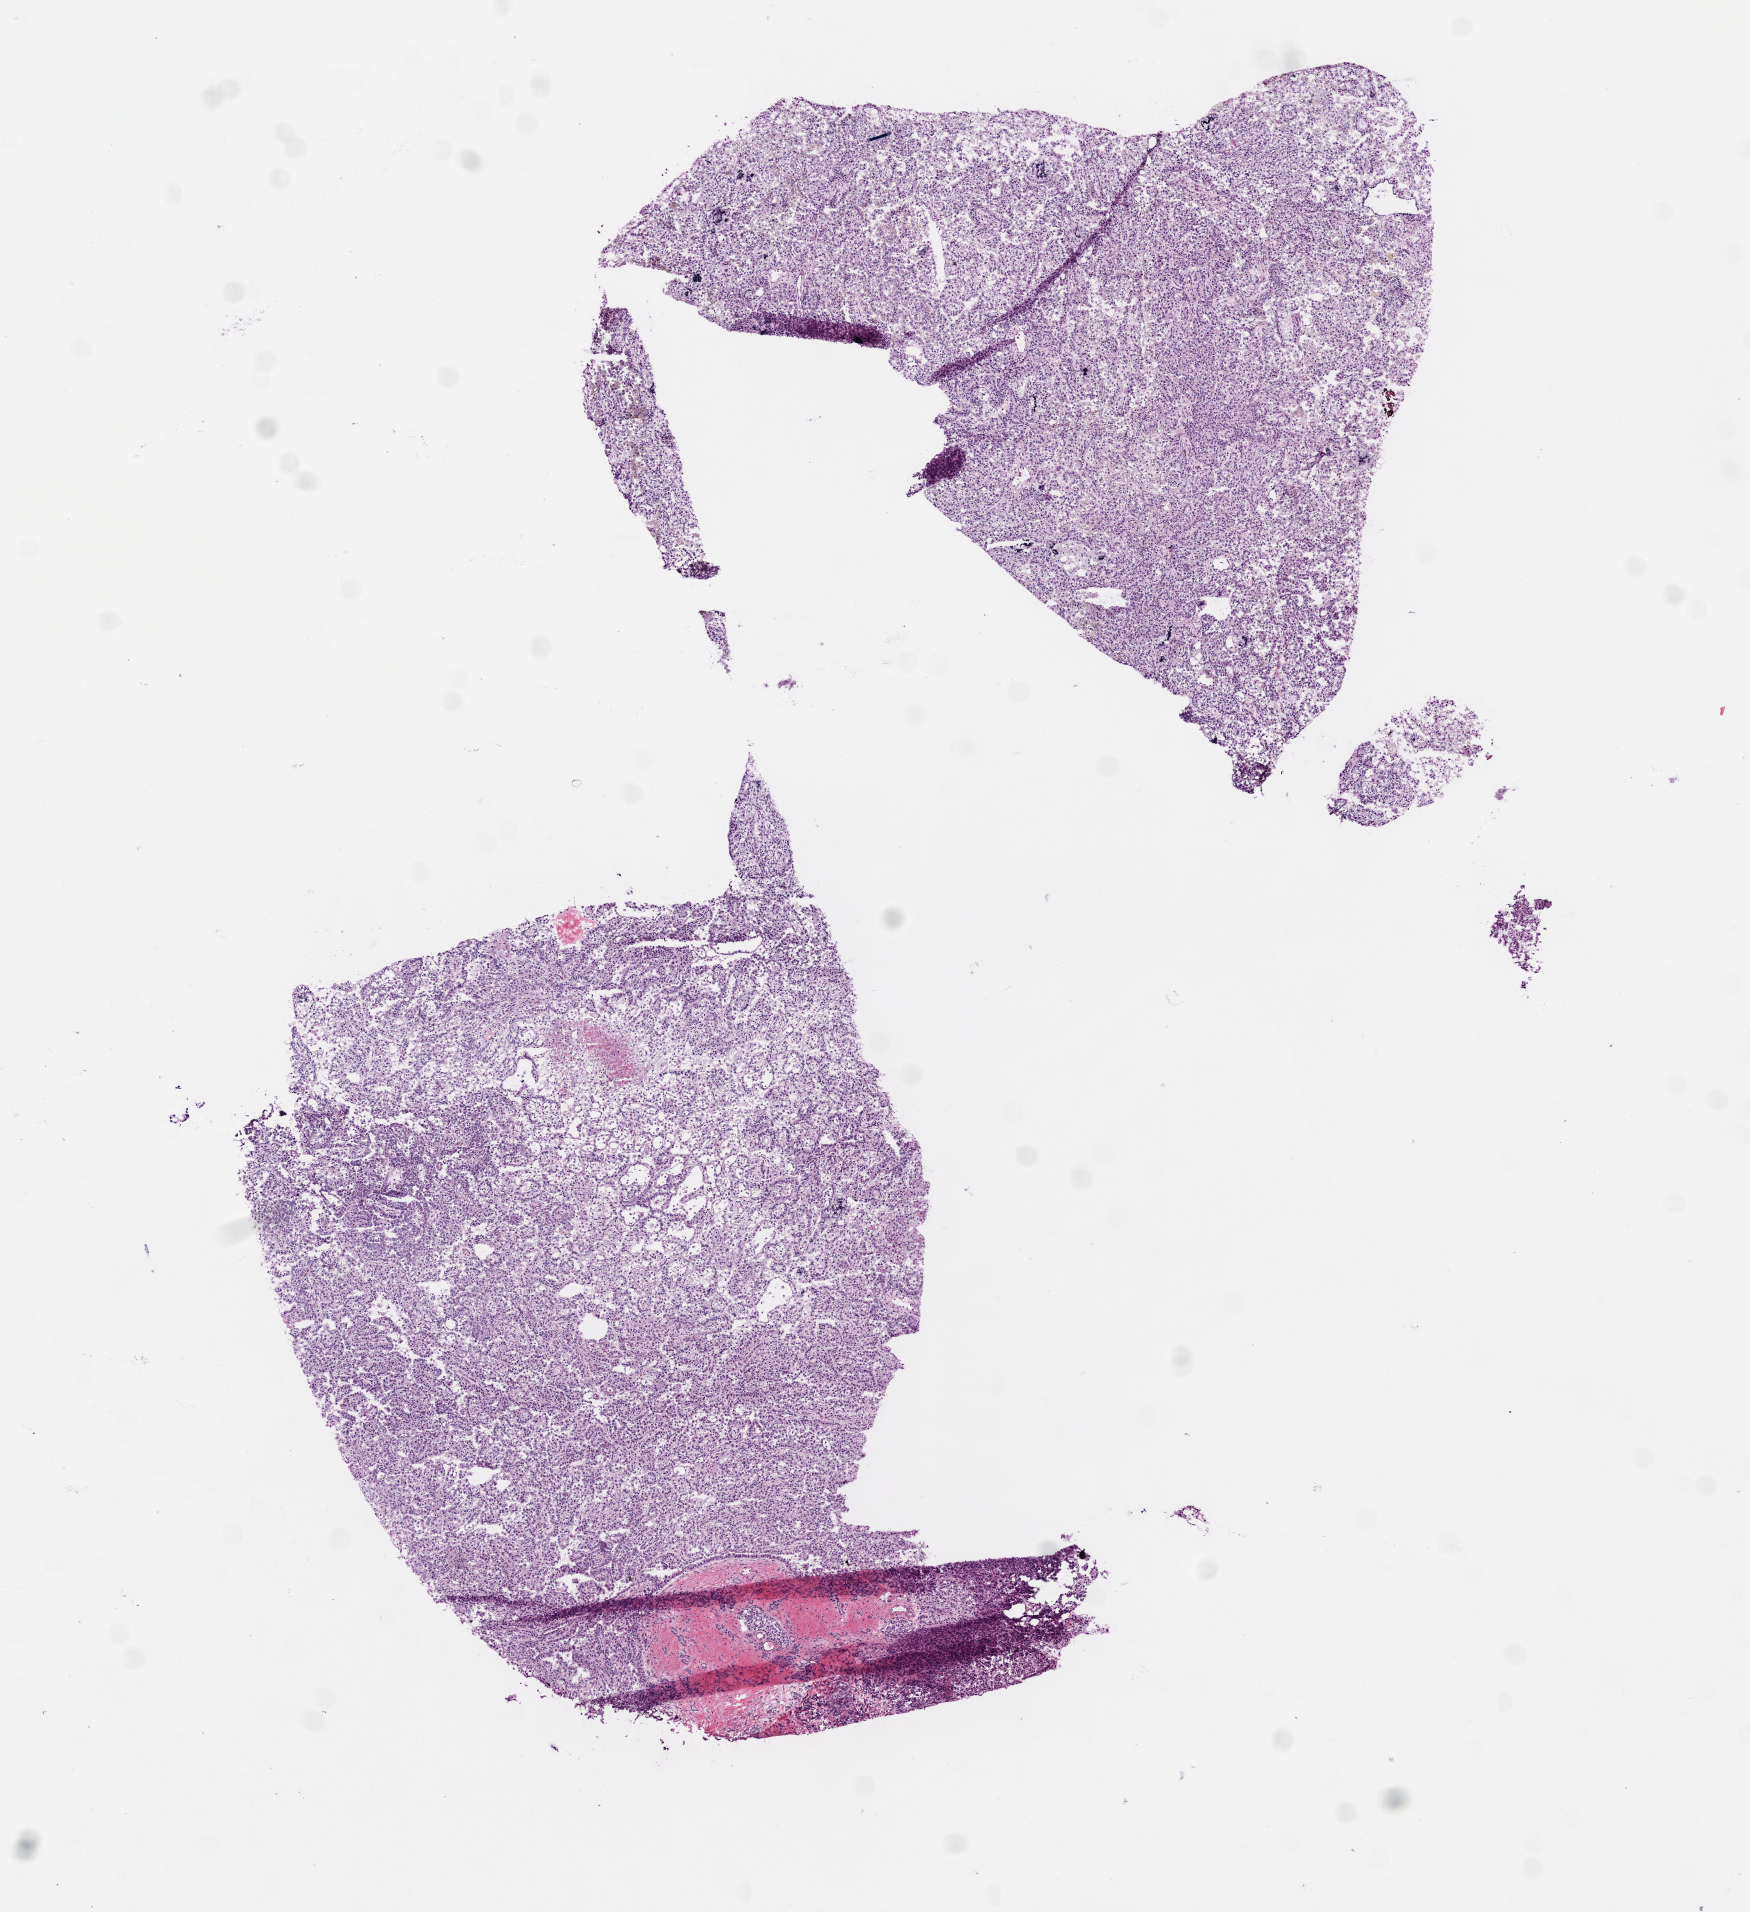
Whole-slide histology image, H&E, shown as a low-resolution overview of the whole scanned area (about 7.0 x 7.7 mm, acquisition: 20x scan), frozen section from the bottom of the tissue portion, sample: primary tumour, kidney. Patient: male, age at initial diagnosis 52 years. Pathologist review of this section (percent, as recorded): tumour cells 95%, tumour nuclei 85%, normal cells 0%, stromal cells 5%, necrosis 0%.
• AJCC pathologic stage: III
• histologic diagnosis: Papillary adenocarcinoma, NOS